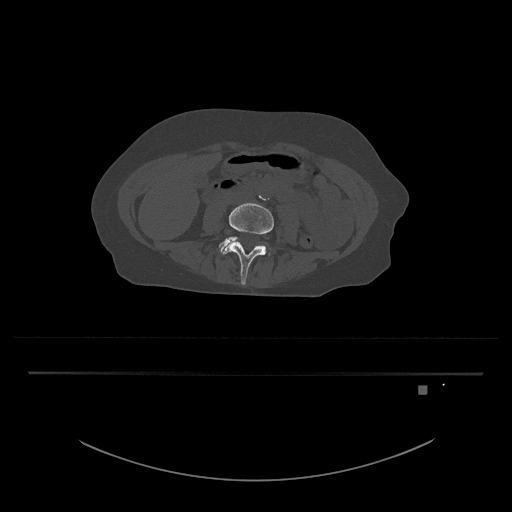
CT including the spine, one axial slice; slice 353 of 797 in the series (ordered by position); reconstruction kernel Br40s/3; 120 kVp; bone window (W 1800 / L 400 HU); 0.5 mm slice thickness; 512 × 512 image matrix, field of view 500 × 500 mm. Female patient, age 57 years. From the clinical record (not read from this slice): primary cancer: cervical.
Structures marked on this image (semi-automatically segmented with operator editing):
- L4 vertebra: bounding box [x1, y1, x2, y2] px = [221, 203, 274, 285]